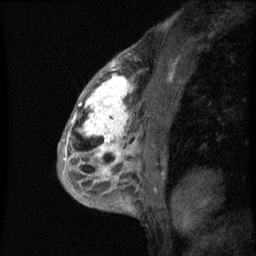
Breast MRI (dynamic contrast-enhanced), one sagittal slice. Slice 36 of 60 in the series (ordered by position). Dynamic contrast-enhanced series, image 2 of 3 at this slice position (ordered by acquisition). 1.5 T. TE 4.2 ms, TR 8 ms. 256 × 256 image matrix, field of view 180 × 180 mm. Patient: female, 50 years.
Outlined on this slice (semi-automatic segmentation, software-assisted and operator-edited):
- analysis volume of interest (the breast-tissue region the enhancement analysis was run in; not a lesion): box from (x=66, y=64) to (x=141, y=187) px
- tumour enhancement mask (voxels above the 70 % enhancement threshold inside the analysis volume of interest): (x=66, y=64)–(x=133, y=173)